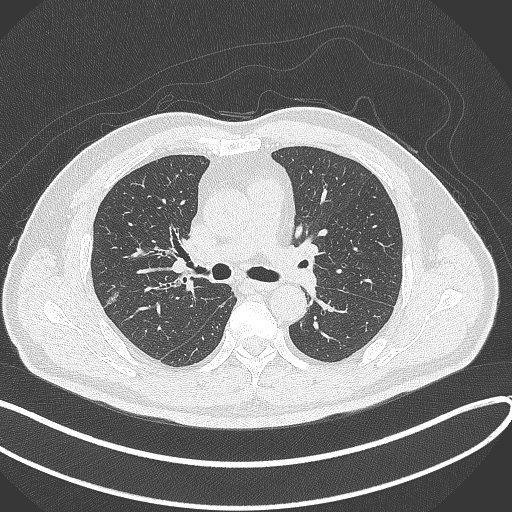
Chest CT, one axial slice; slice 207 of 372 in the series (ordered by position); reconstruction kernel B70f; lung window (W 1500 / L -600 HU); 1 mm slice thickness; 512 × 512 image matrix, field of view 400 × 400 mm. Patient: male, 60 years. From the clinical record (not read from this slice): clinical TNM (as recorded): T1c N0 M0.
Structures marked on this image (rectangle marked by the reading radiologist):
- lung tumour (recorded histology: adenocarcinoma): bounding box [x1, y1, x2, y2] px = [101, 283, 126, 311]